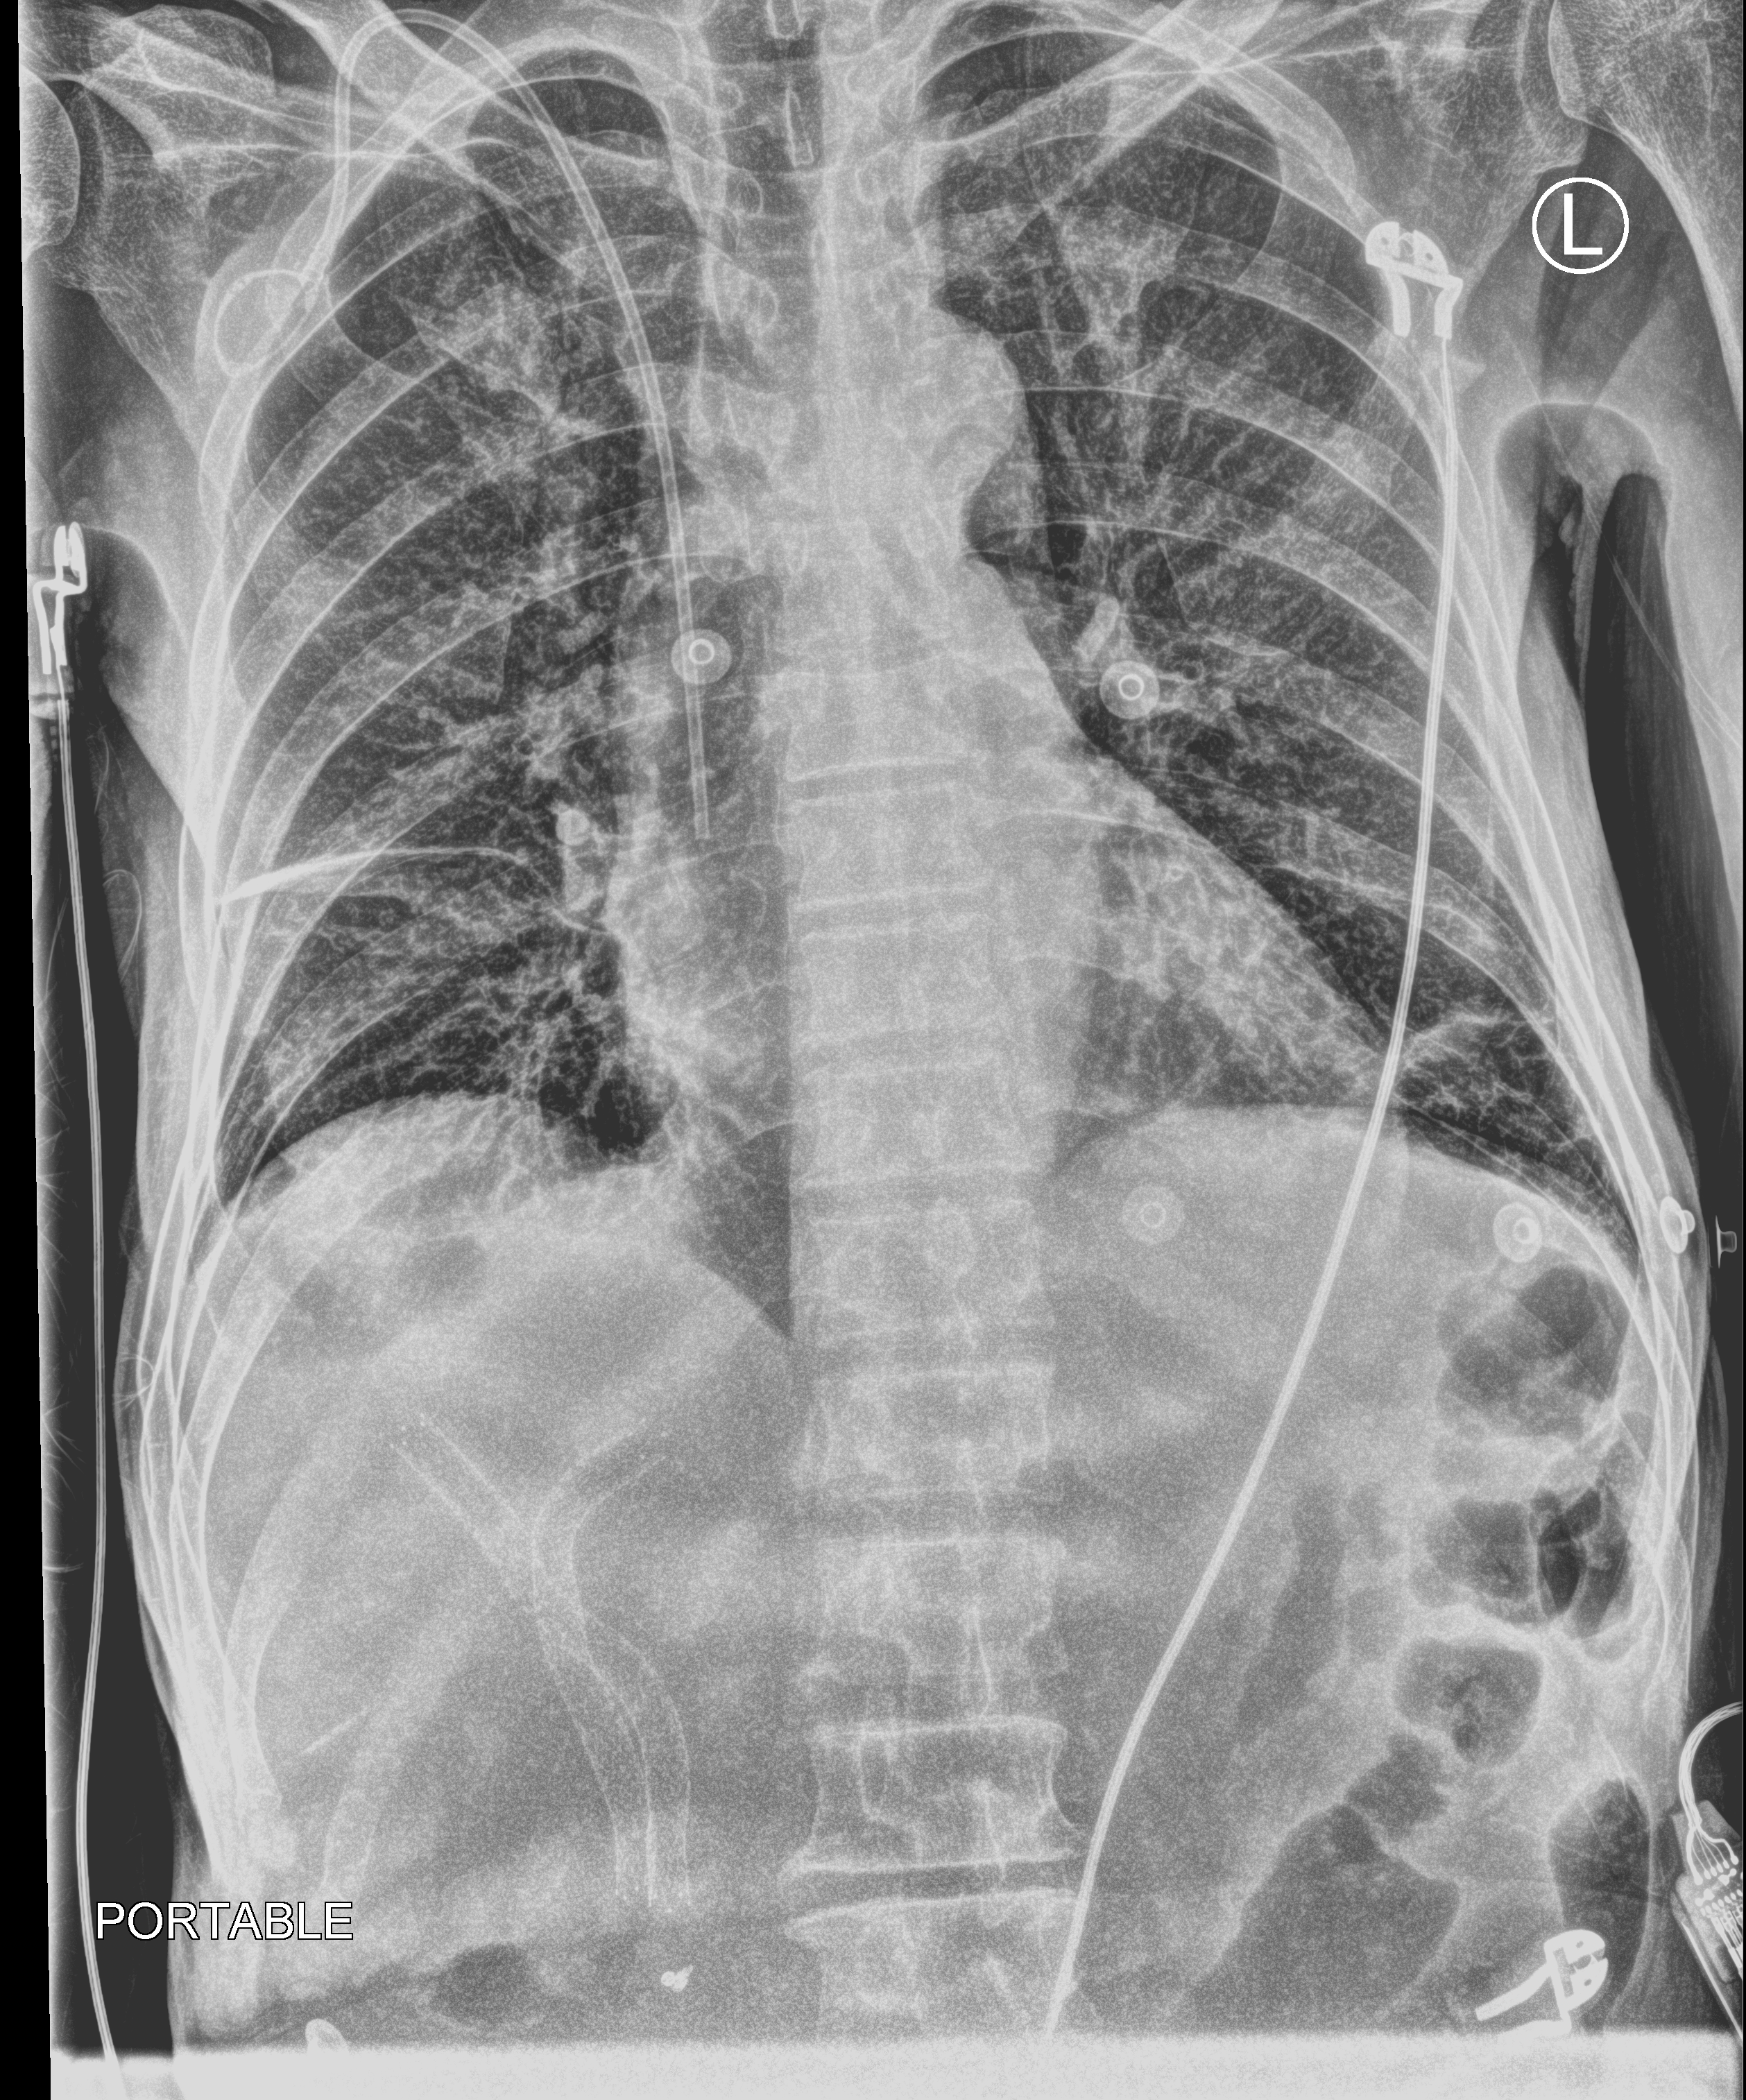
Portable chest radiograph; anteroposterior (AP) projection. Patient hospitalised with COVID-19; male, aged 60–74 years.
Hospital-stay facts (about this admission, not read from this image; timing relative to this image not recorded): admitted to intensive care during this hospital stay: no.